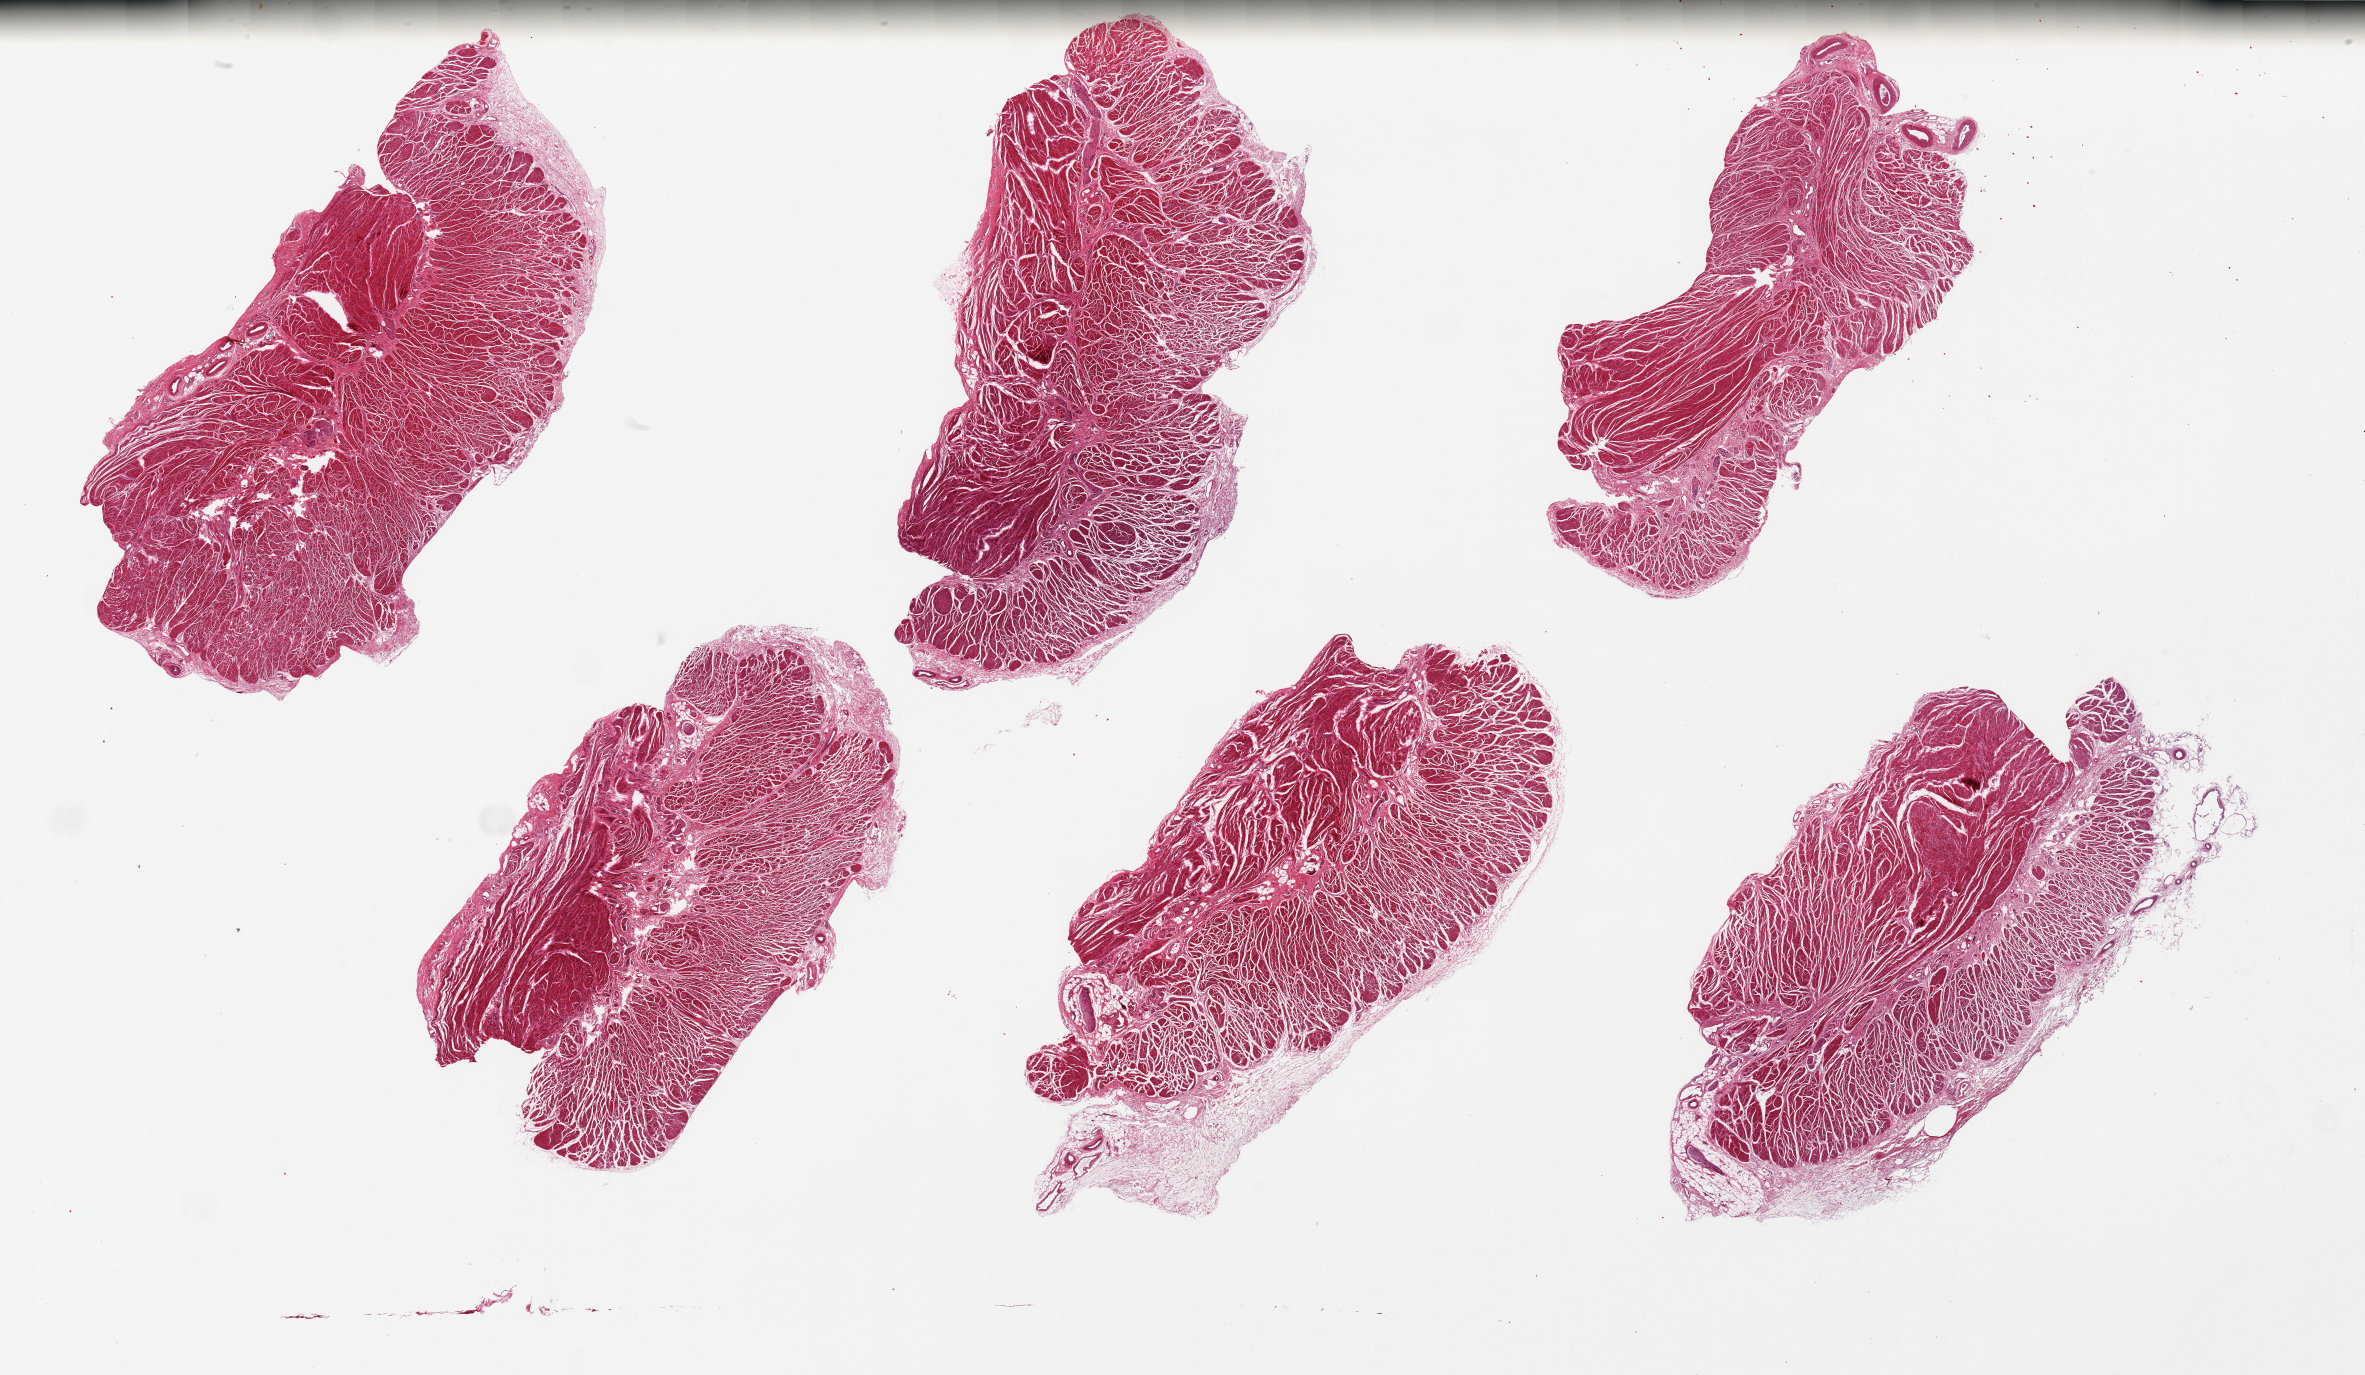
Whole-slide image, hematoxylin and eosin (H&E) stain, brightfield, shown as a low-resolution overview of the whole scanned area (about 37.4 x 21.7 mm, from a 20x scan). PAXgene-fixed paraffin-embedded (PFPE) section. Target tissue: gastroesophageal junction. Tissue donor sample. Donor: male.
Pathologist's review note for this sample: 6 pieces; good specimens, muscularis only.